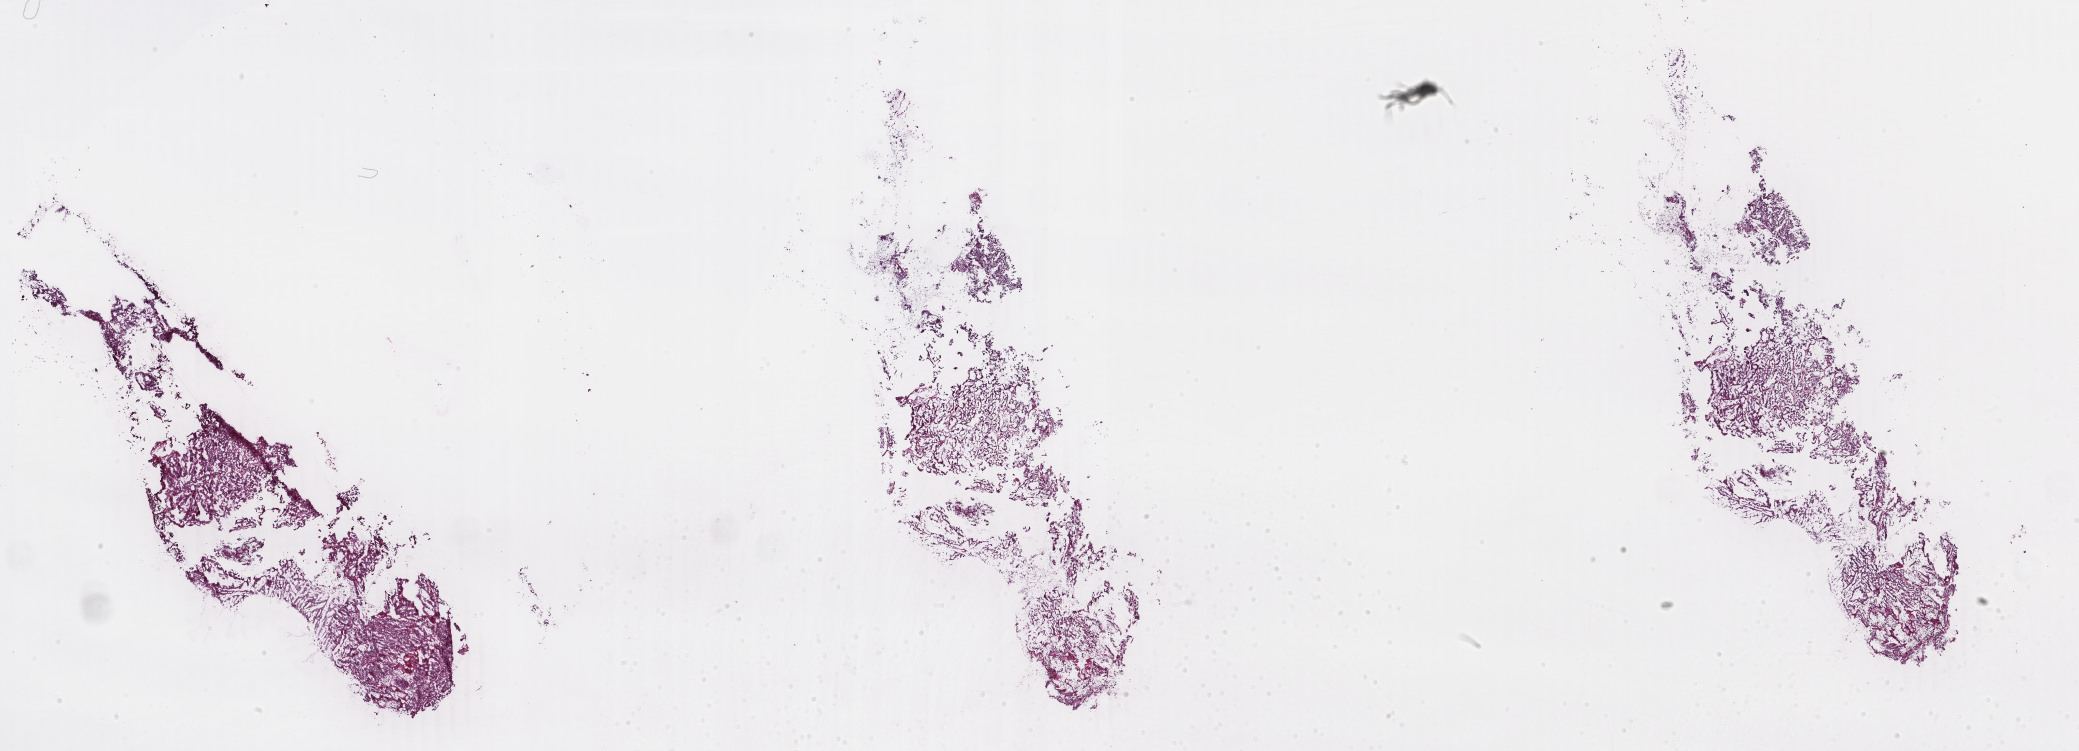
Hematoxylin and eosin (H&E) stained whole-slide image, whole scanned area (about 33.1 x 11.9 mm, from a 40x scan) shown as a low-resolution overview, frozen section, primary tumour sample from the uterus. Patient: female, age at initial diagnosis 56 years. Composition of this section per pathologist review: tumour cells 90%, tumour nuclei 90%.
Pathologic diagnosis: Endometrioid adenocarcinoma, NOS (endometrium).